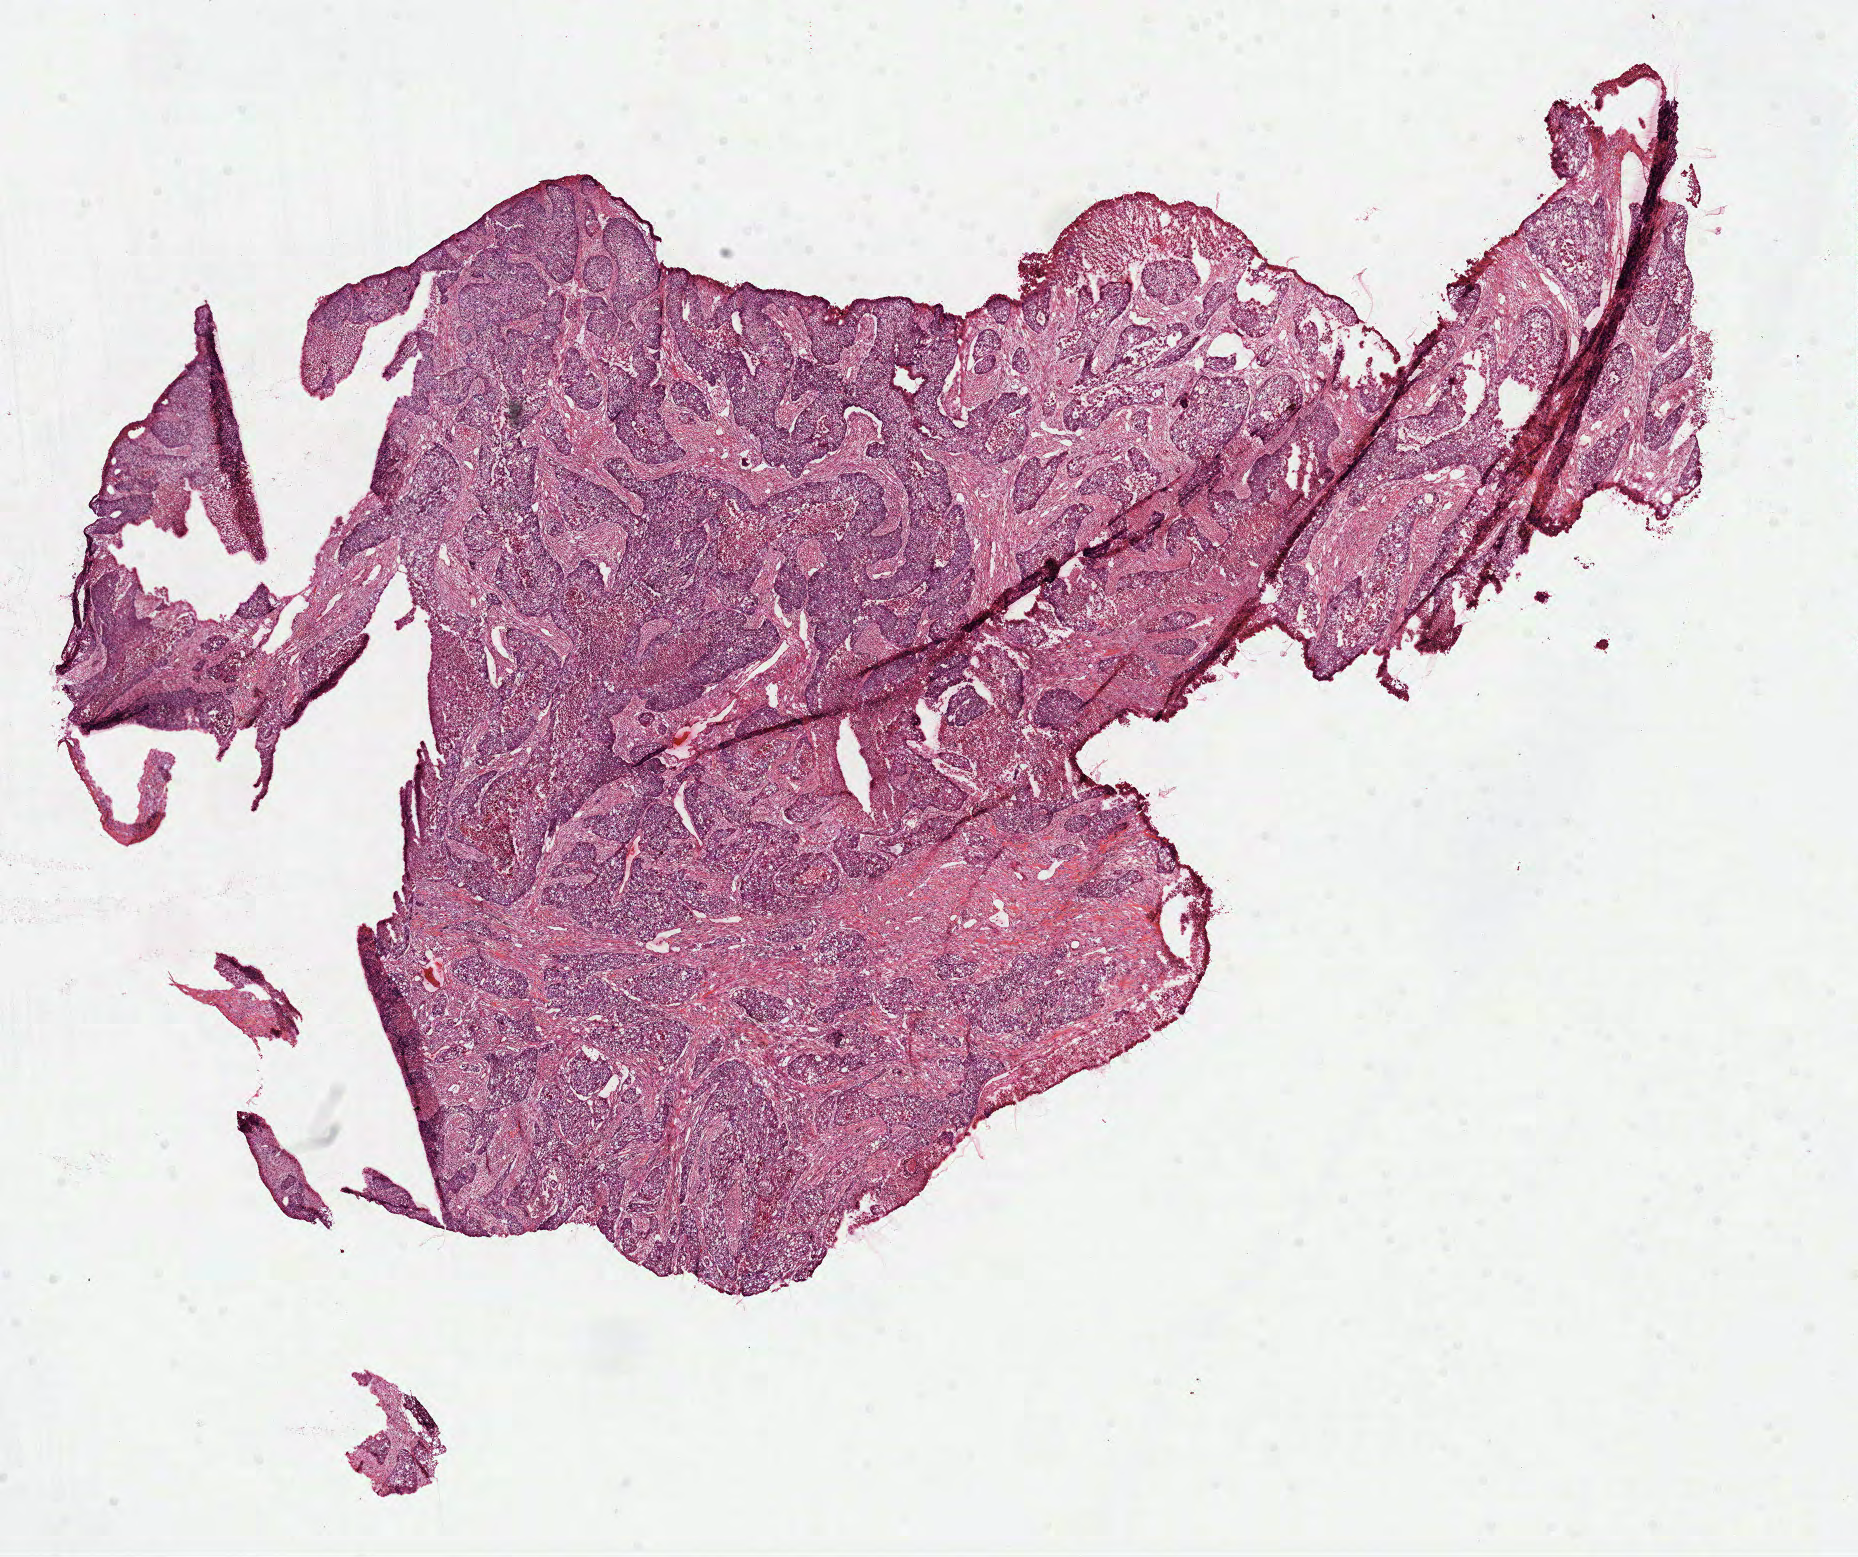
Whole-slide histology image, H&E, a low-resolution overview of the entire scanned area, about 15.0 x 12.6 mm (slide scanned at 40x). Formalin-fixed paraffin-embedded (FFPE) diagnostic section. Primary tumour sample from the lung. Patient: male, age at initial diagnosis 69 years.
Diagnosis: Squamous cell carcinoma, NOS (lower lobe, lung).